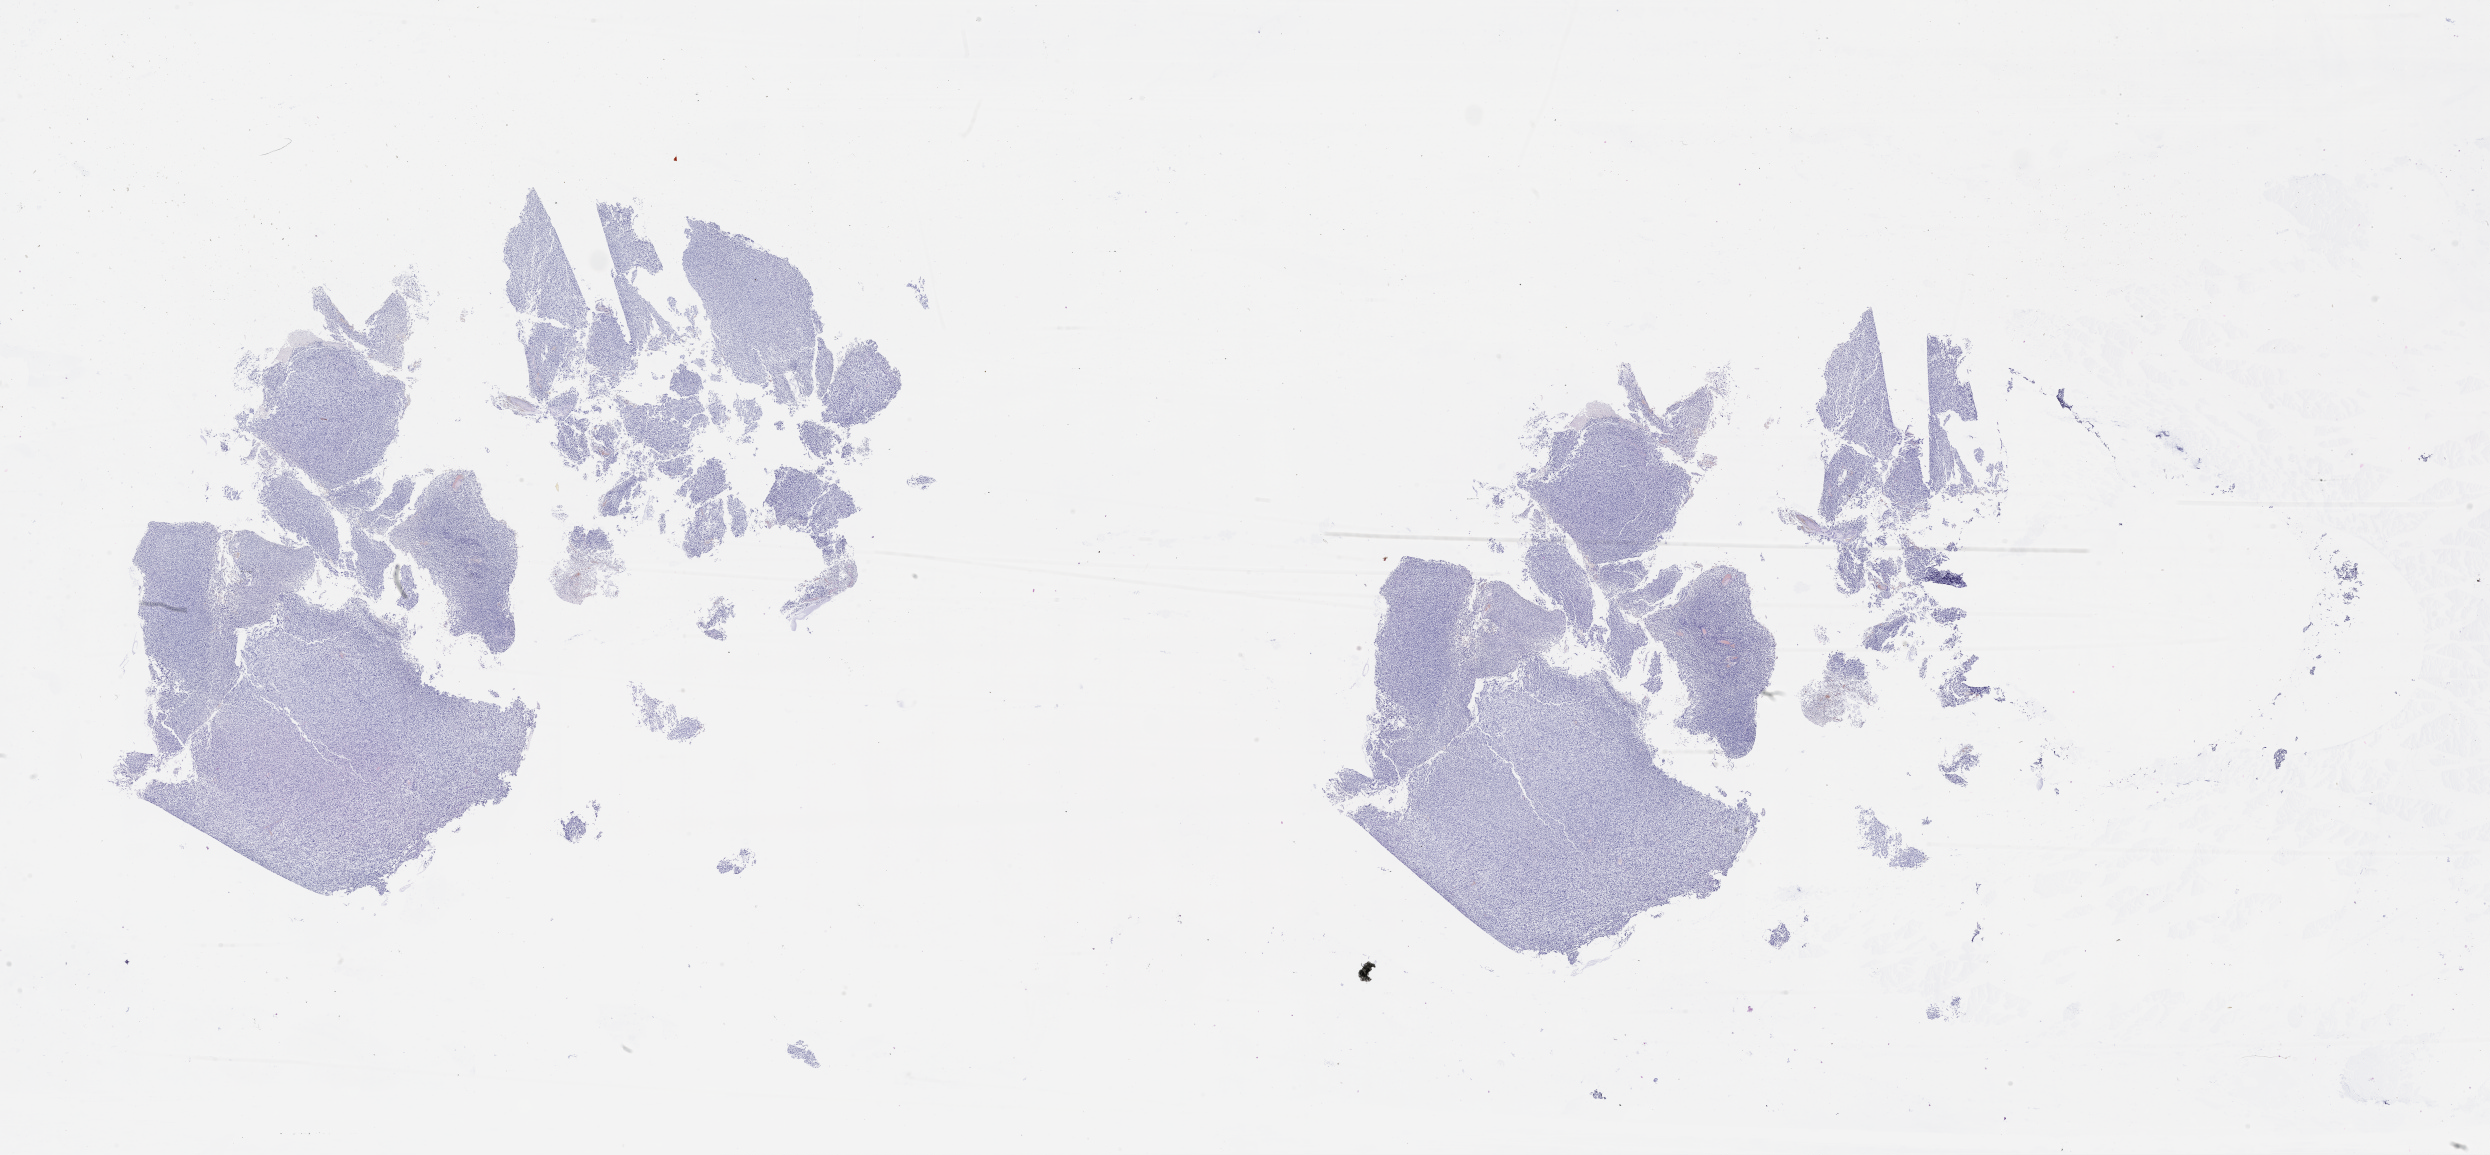
Whole-slide histology image, Hematoxylin and eosin (H&E) stained, low-resolution overview of the scanned area, about 40.1 x 18.6 mm; brain, tumour tissue. 36-year-old male patient.
Histologic diagnosis: Glioblastoma.